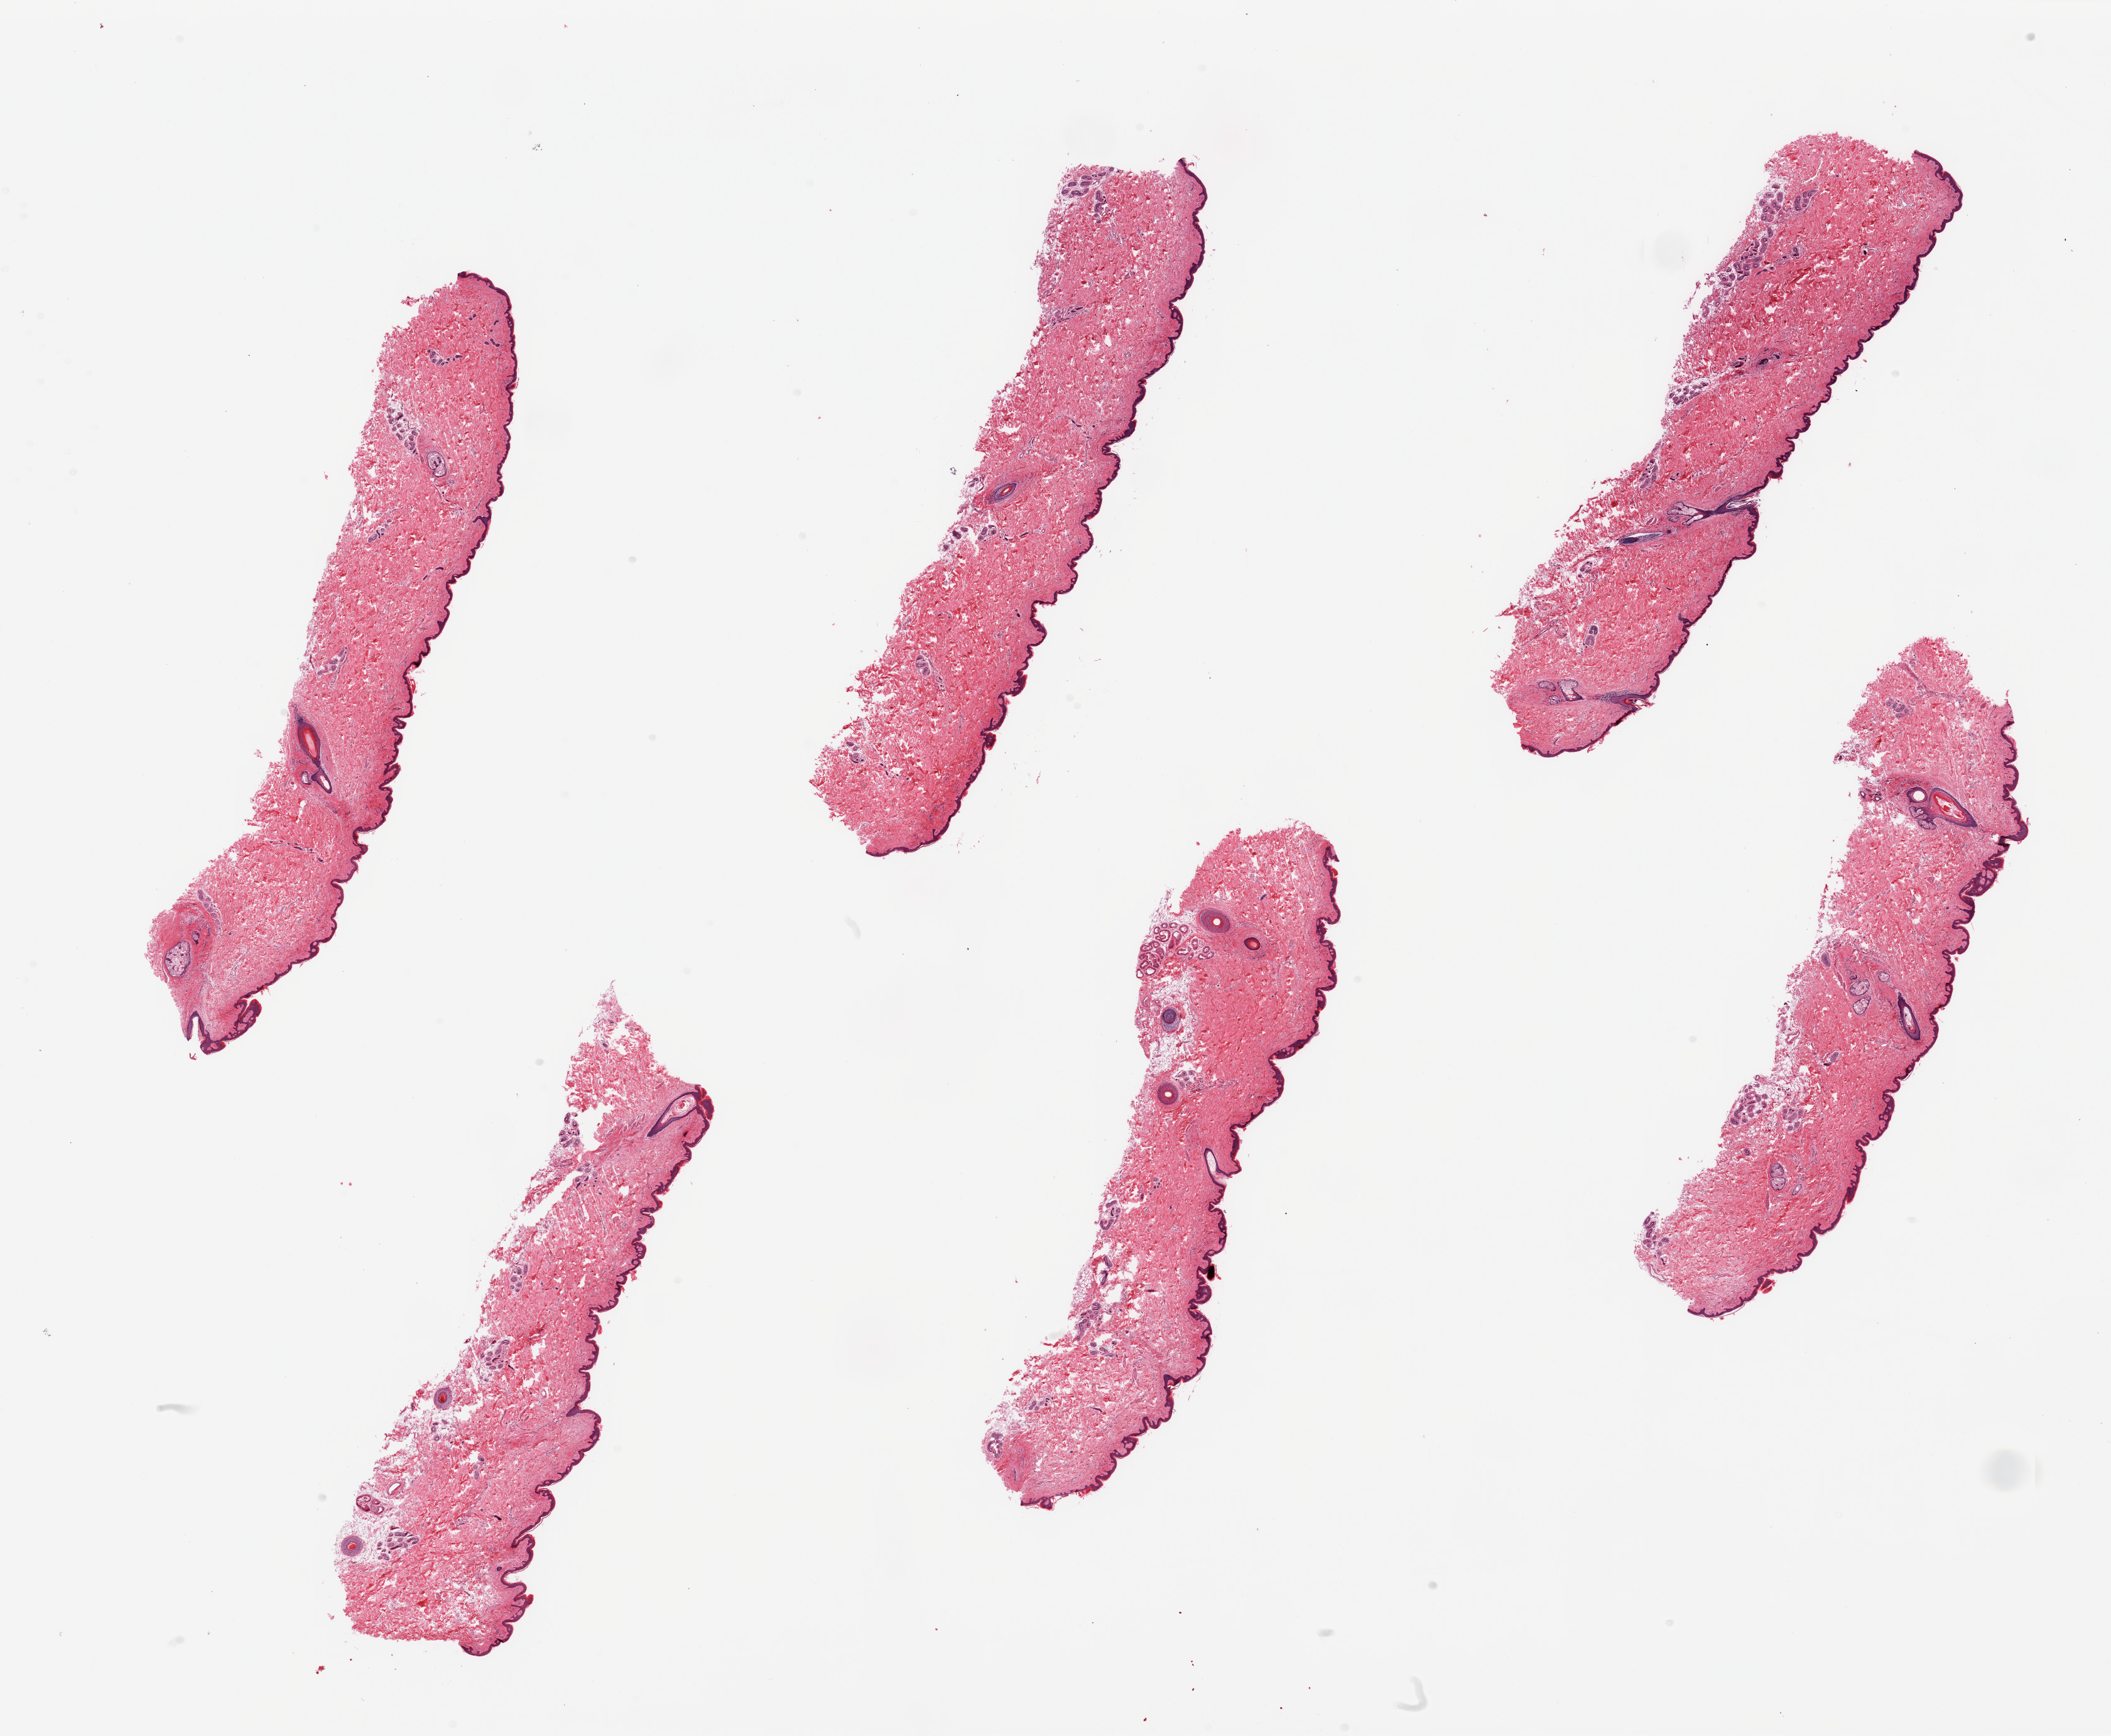
Digitized H&E-stained section — shown as a low-resolution overview of the whole scanned area (about 26.6 x 21.9 mm, acquisition: 20x scan). PAXgene-fixed, paraffin-embedded tissue. Sampled site (target tissue): skin of suprapubic region. Tissue donor sample. Donor: female.
* review note (as recorded): 6 pieces; well trimmed; 1% dermal fat